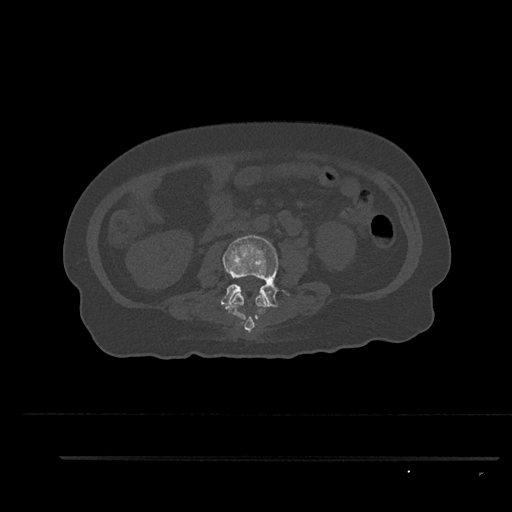
CT including the spine, one axial slice; position 111 of 797 along the scan axis; reconstruction kernel Br40s/3; 120 kVp; bone window (W 1800 / L 400 HU); 0.5 mm slice thickness; 512 × 512 image matrix. Female patient, age 44 years. From the clinical record (not read from this slice): primary cancer: renal.
Outlined on this slice (semi-automatically segmented with operator editing):
- L2 vertebra: box from (x=226, y=293) to (x=267, y=333) px
- L3 vertebra: (x=220, y=235)–(x=290, y=309)